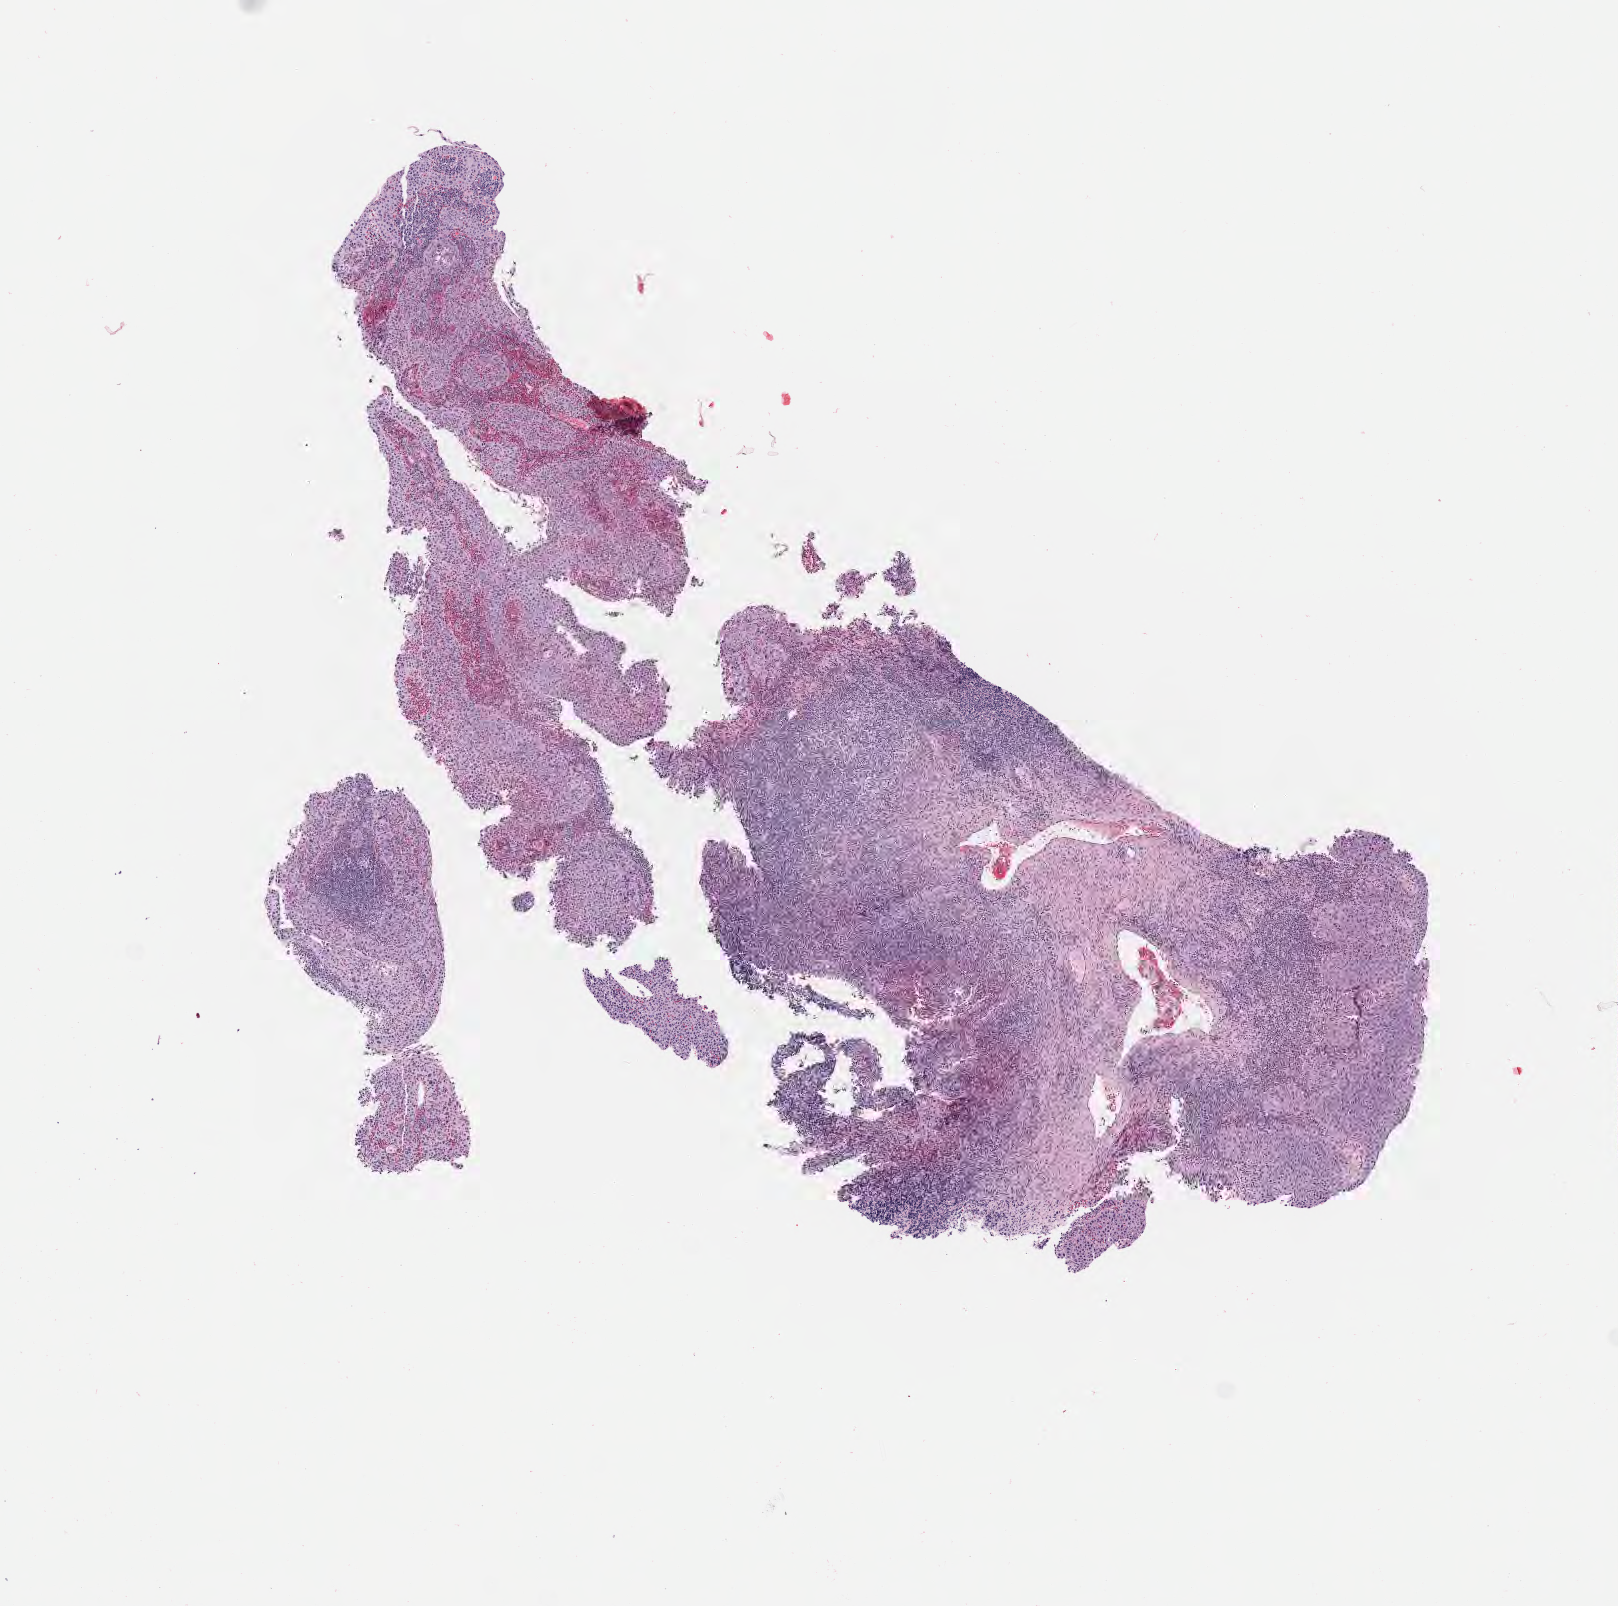
Hematoxylin and eosin (H&E) whole-slide image — low-resolution overview of the scanned area, about 6.5 x 6.5 mm; specimen: tumor tissue; site: cervix. Patient: female, aged 52.
Diagnosis: Squamous cell carcinoma, large cell, nonkeratinizing, NOS.